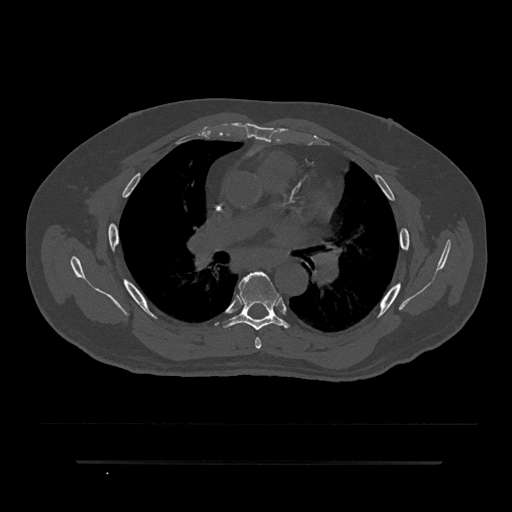
CT including the spine, one axial slice; position 534 of 797 along the scan axis; reconstruction kernel Br40s/3; 120 kVp; bone window (W 1800 / L 400 HU); 0.5 mm slice thickness; 512 × 512 image matrix, field of view 464 × 464 mm. Patient: male, 59 years. Case-level facts recorded for this patient, not image findings: primary cancer: bile ducts.
Structures marked on this image (semi-automatic segmentation, software-assisted and operator-edited):
- T5 vertebra: bounding box <255,337,262,349> (left, top, right, bottom; pixels)
- T6 vertebra: <223,271,290,331>